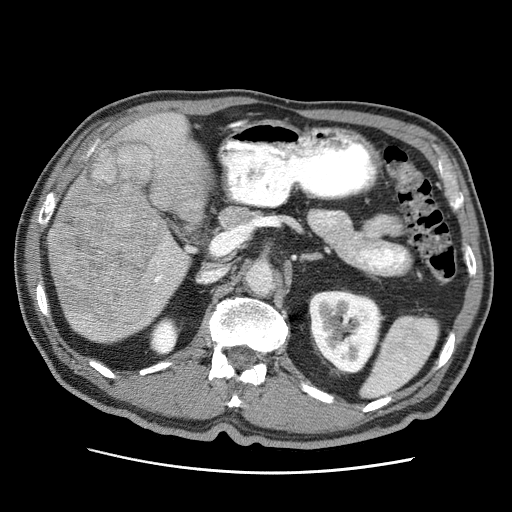
Contrast-enhanced abdominal CT (liver protocol), one axial slice; position 19 of 75 along the scan axis; reconstruction kernel STANDARD; soft-tissue window (W 400 / L 40 HU); 2.5 mm slice thickness; 512 × 512 image matrix, field of view 360 × 360 mm. From the clinical record (not read from this slice): diagnosis: hepatocellular carcinoma (patient treated with transarterial chemoembolisation; whether this scan precedes or follows treatment is not stated here); TNM stage (as recorded): Stage-IIIA; Child-Pugh class: A; tumour differentiation: well differentiated; tumour nodularity: multinodular.
Structures marked on this image (semi-automatic segmentation, software-assisted and operator-edited):
- liver parenchyma outside the tumour (the mass and vessels are separate outlines, so this box may not span the whole liver): bounding box <48,112,208,342> (left, top, right, bottom; pixels)
- mass: <50,143,160,324>
- liver vessels: <75,125,181,324>